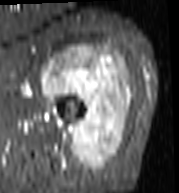
MRI of an extremity soft-tissue mass, one axial slice. Slice 75 of 103 in the series (ordered by position). STIR. MR volume resampled by the dataset authors to the PET/CT grid (not the native acquisition matrix). 3.27 mm slice thickness. 179 × 193 image matrix, field of view 175 × 188 mm. Female patient. Case-level facts recorded for this patient, not image findings: histological type: undifferentiated – high grade; grade: high; site of the primary tumour: left thigh.
Annotated regions visible in this slice (expert contour drawn on MRI and transferred to this co-registered scan by the dataset authors):
- gross tumour volume including surrounding oedema: bounding box <41,46,133,170> (left, top, right, bottom; pixels)
- gross tumour volume (mass): <41,46,133,170>